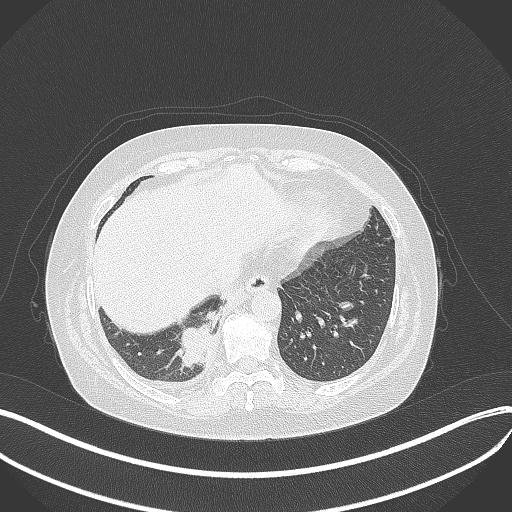
Chest CT, one axial slice; slice 94 of 381 in the series (ordered by position); 120 kVp; lung window (W 1500 / L -600 HU); 1 mm slice thickness; 512 × 512 image matrix, field of view 400 × 400 mm. Female patient, age 56 years. Case-level facts recorded for this patient, not image findings: clinical TNM (as recorded): T2b N1 M0; histopathological grade: G3.
Annotated regions visible in this slice (bounding box drawn by a radiologist):
- lung tumour (recorded histology: small cell carcinoma): bounding box (x1, y1, x2, y2) in pixels: (169, 308, 220, 368)